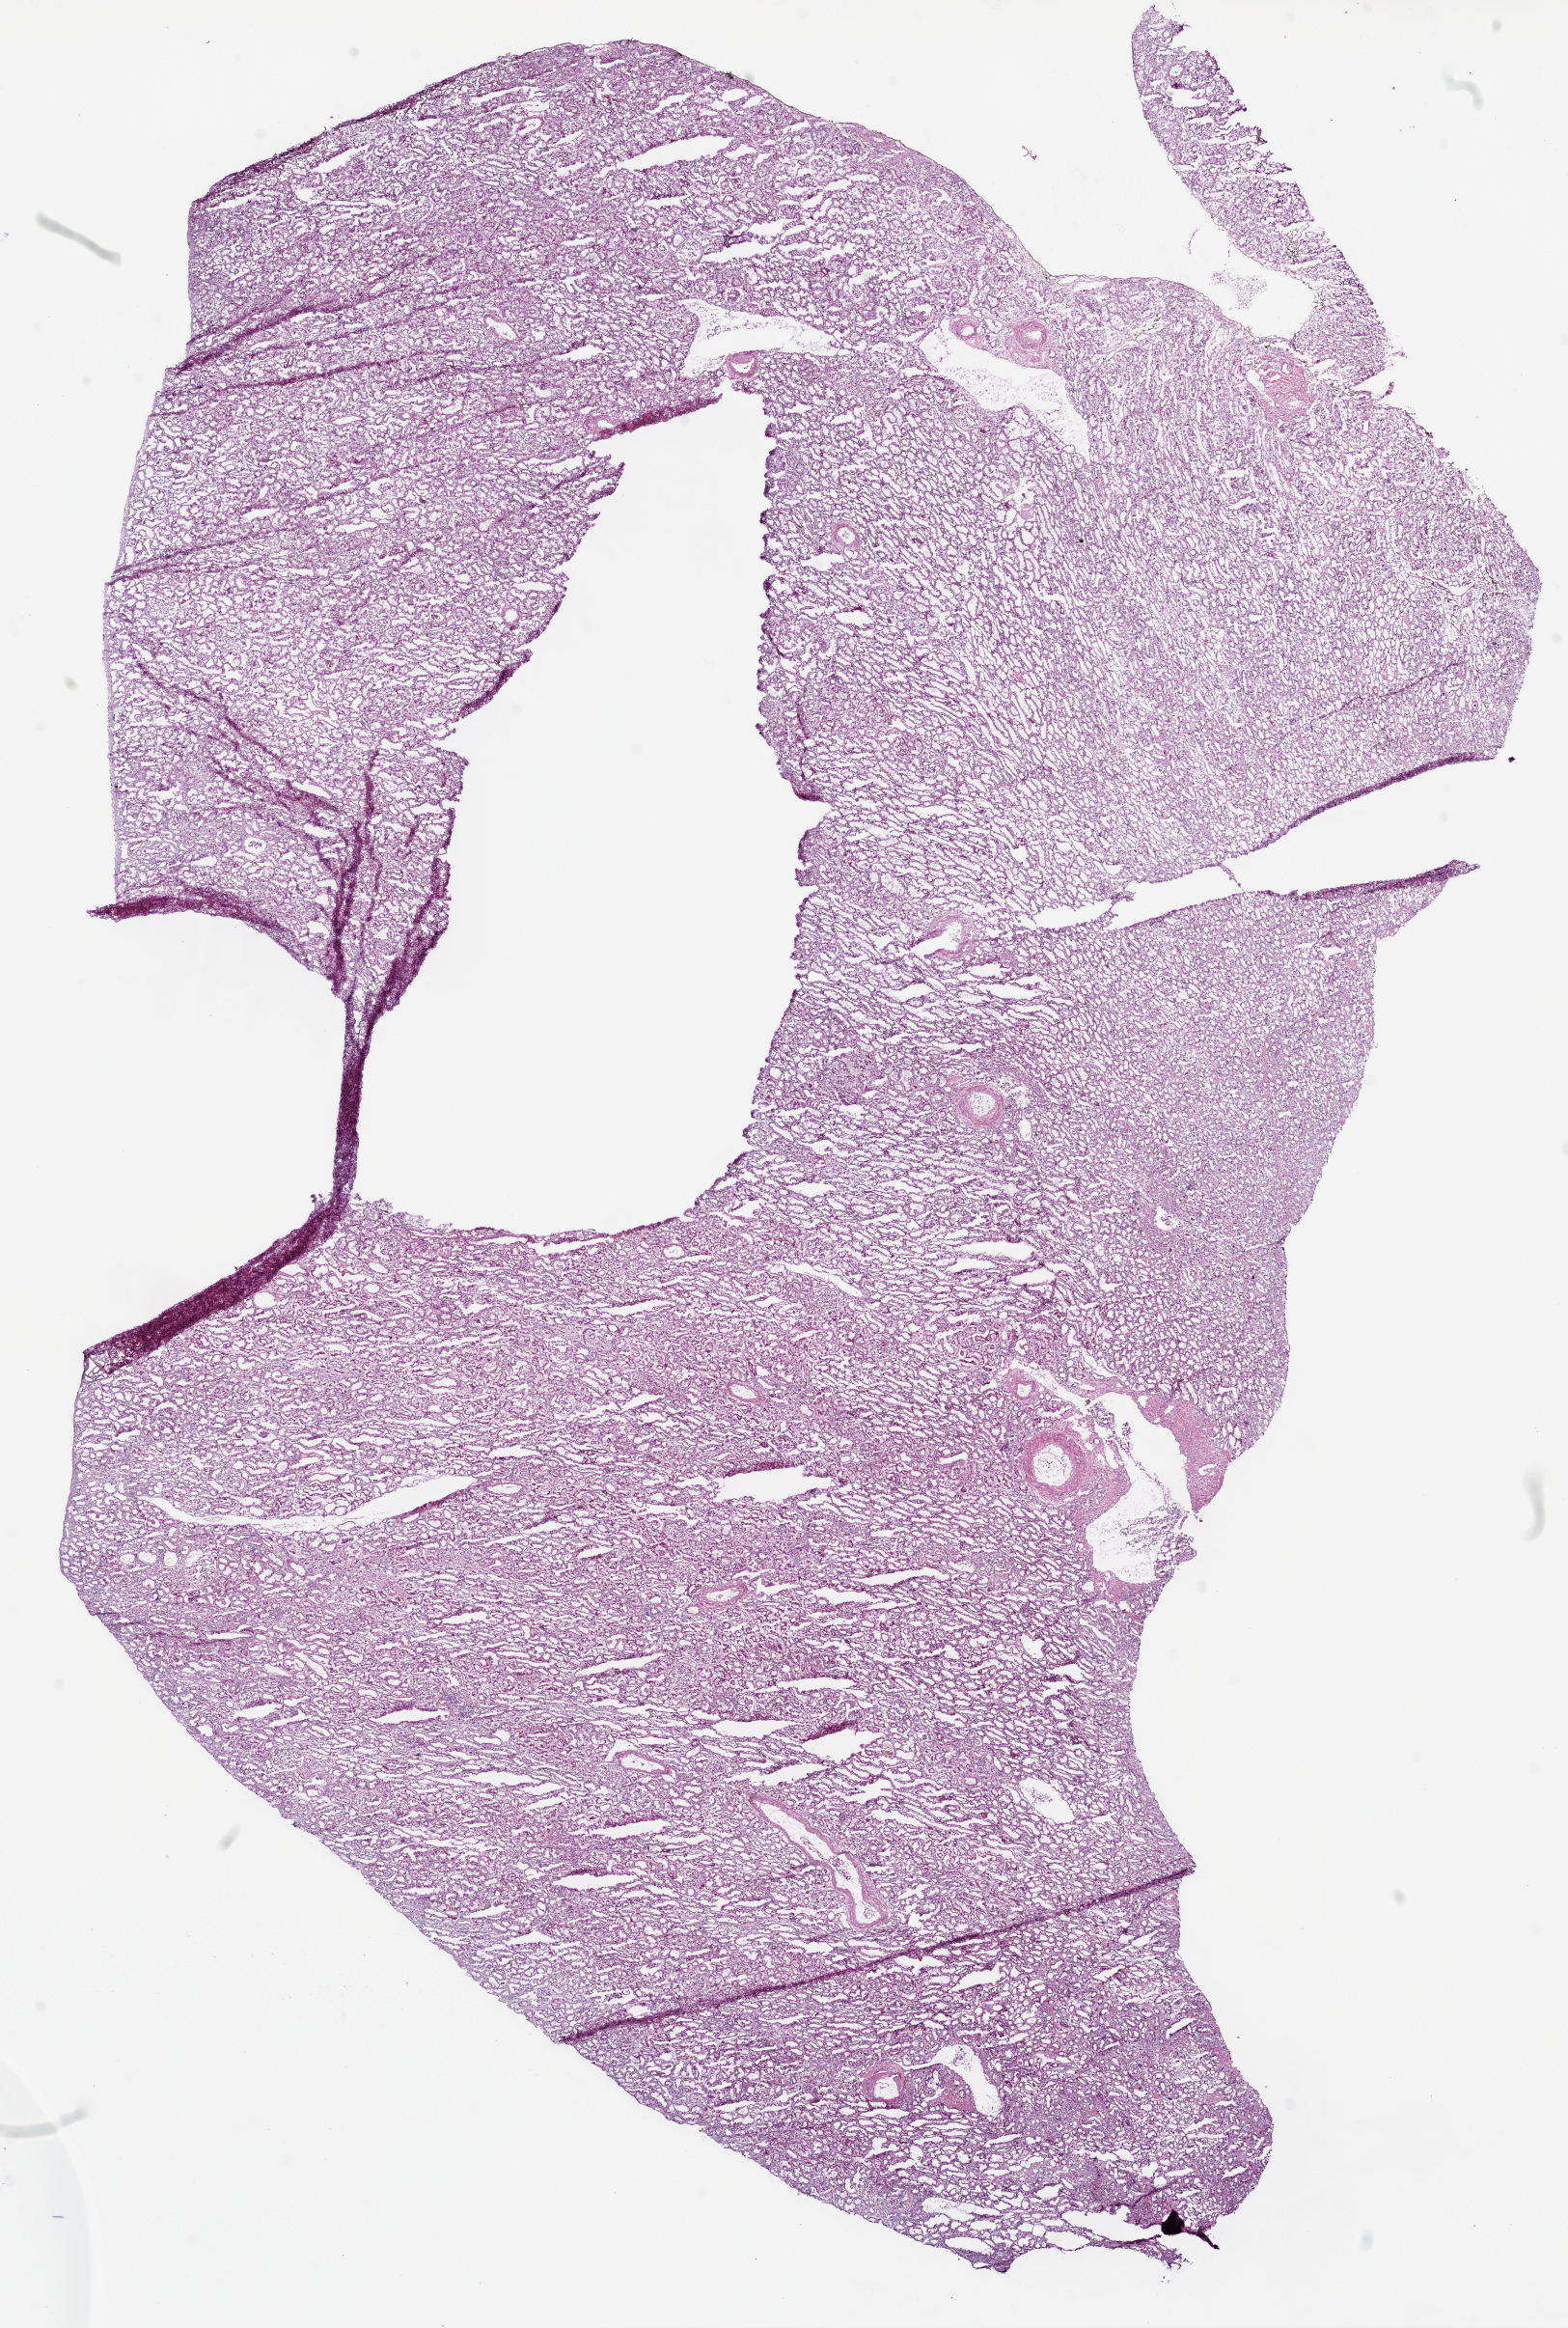
H&E whole-slide image, low-resolution overview of the scanned area, about 13.0 x 19.4 mm; frozen section from the bottom of the tissue portion; kidney, solid tissue normal (non-tumour tissue) sample. Patient: female, age at initial diagnosis 53 years.
This section: solid tissue normal sample (biorepository sample class). Patient diagnosis: Clear cell adenocarcinoma, NOS.